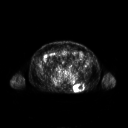
FDG PET of an extremity soft-tissue mass (from a PET/CT study), one axial slice. Slice 88 of 267 in the series (ordered by position). 3.27 mm slice thickness. 128 × 128 image matrix, field of view 700 × 700 mm. Patient: male, 61 years. From the clinical record (not read from this slice): histological type: pleiomorphic leiomyosarcoma; grade: high; site of the primary tumour: left buttock.
Structures marked on this image (expert contour drawn on MRI and transferred to this co-registered scan by the dataset authors):
- gross tumour volume including surrounding oedema: bounding box (x1, y1, x2, y2) in pixels: (73, 83, 84, 91)
- gross tumour volume (mass): (73, 84, 84, 91)